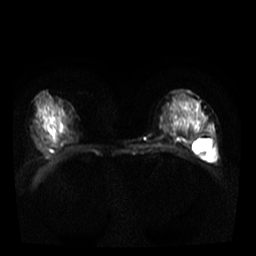
Breast MRI, one axial slice. Diffusion-weighted series; image 2 of 4 stored at this slice position (different b-values; order by instance number). 3 T. 5 mm slice thickness. 256 × 256 image matrix. Female patient.
Annotated regions visible in this slice (manually delineated by an expert):
- tumour on diffusion-weighted imaging: bounding box <200,153,217,162> (left, top, right, bottom; pixels)